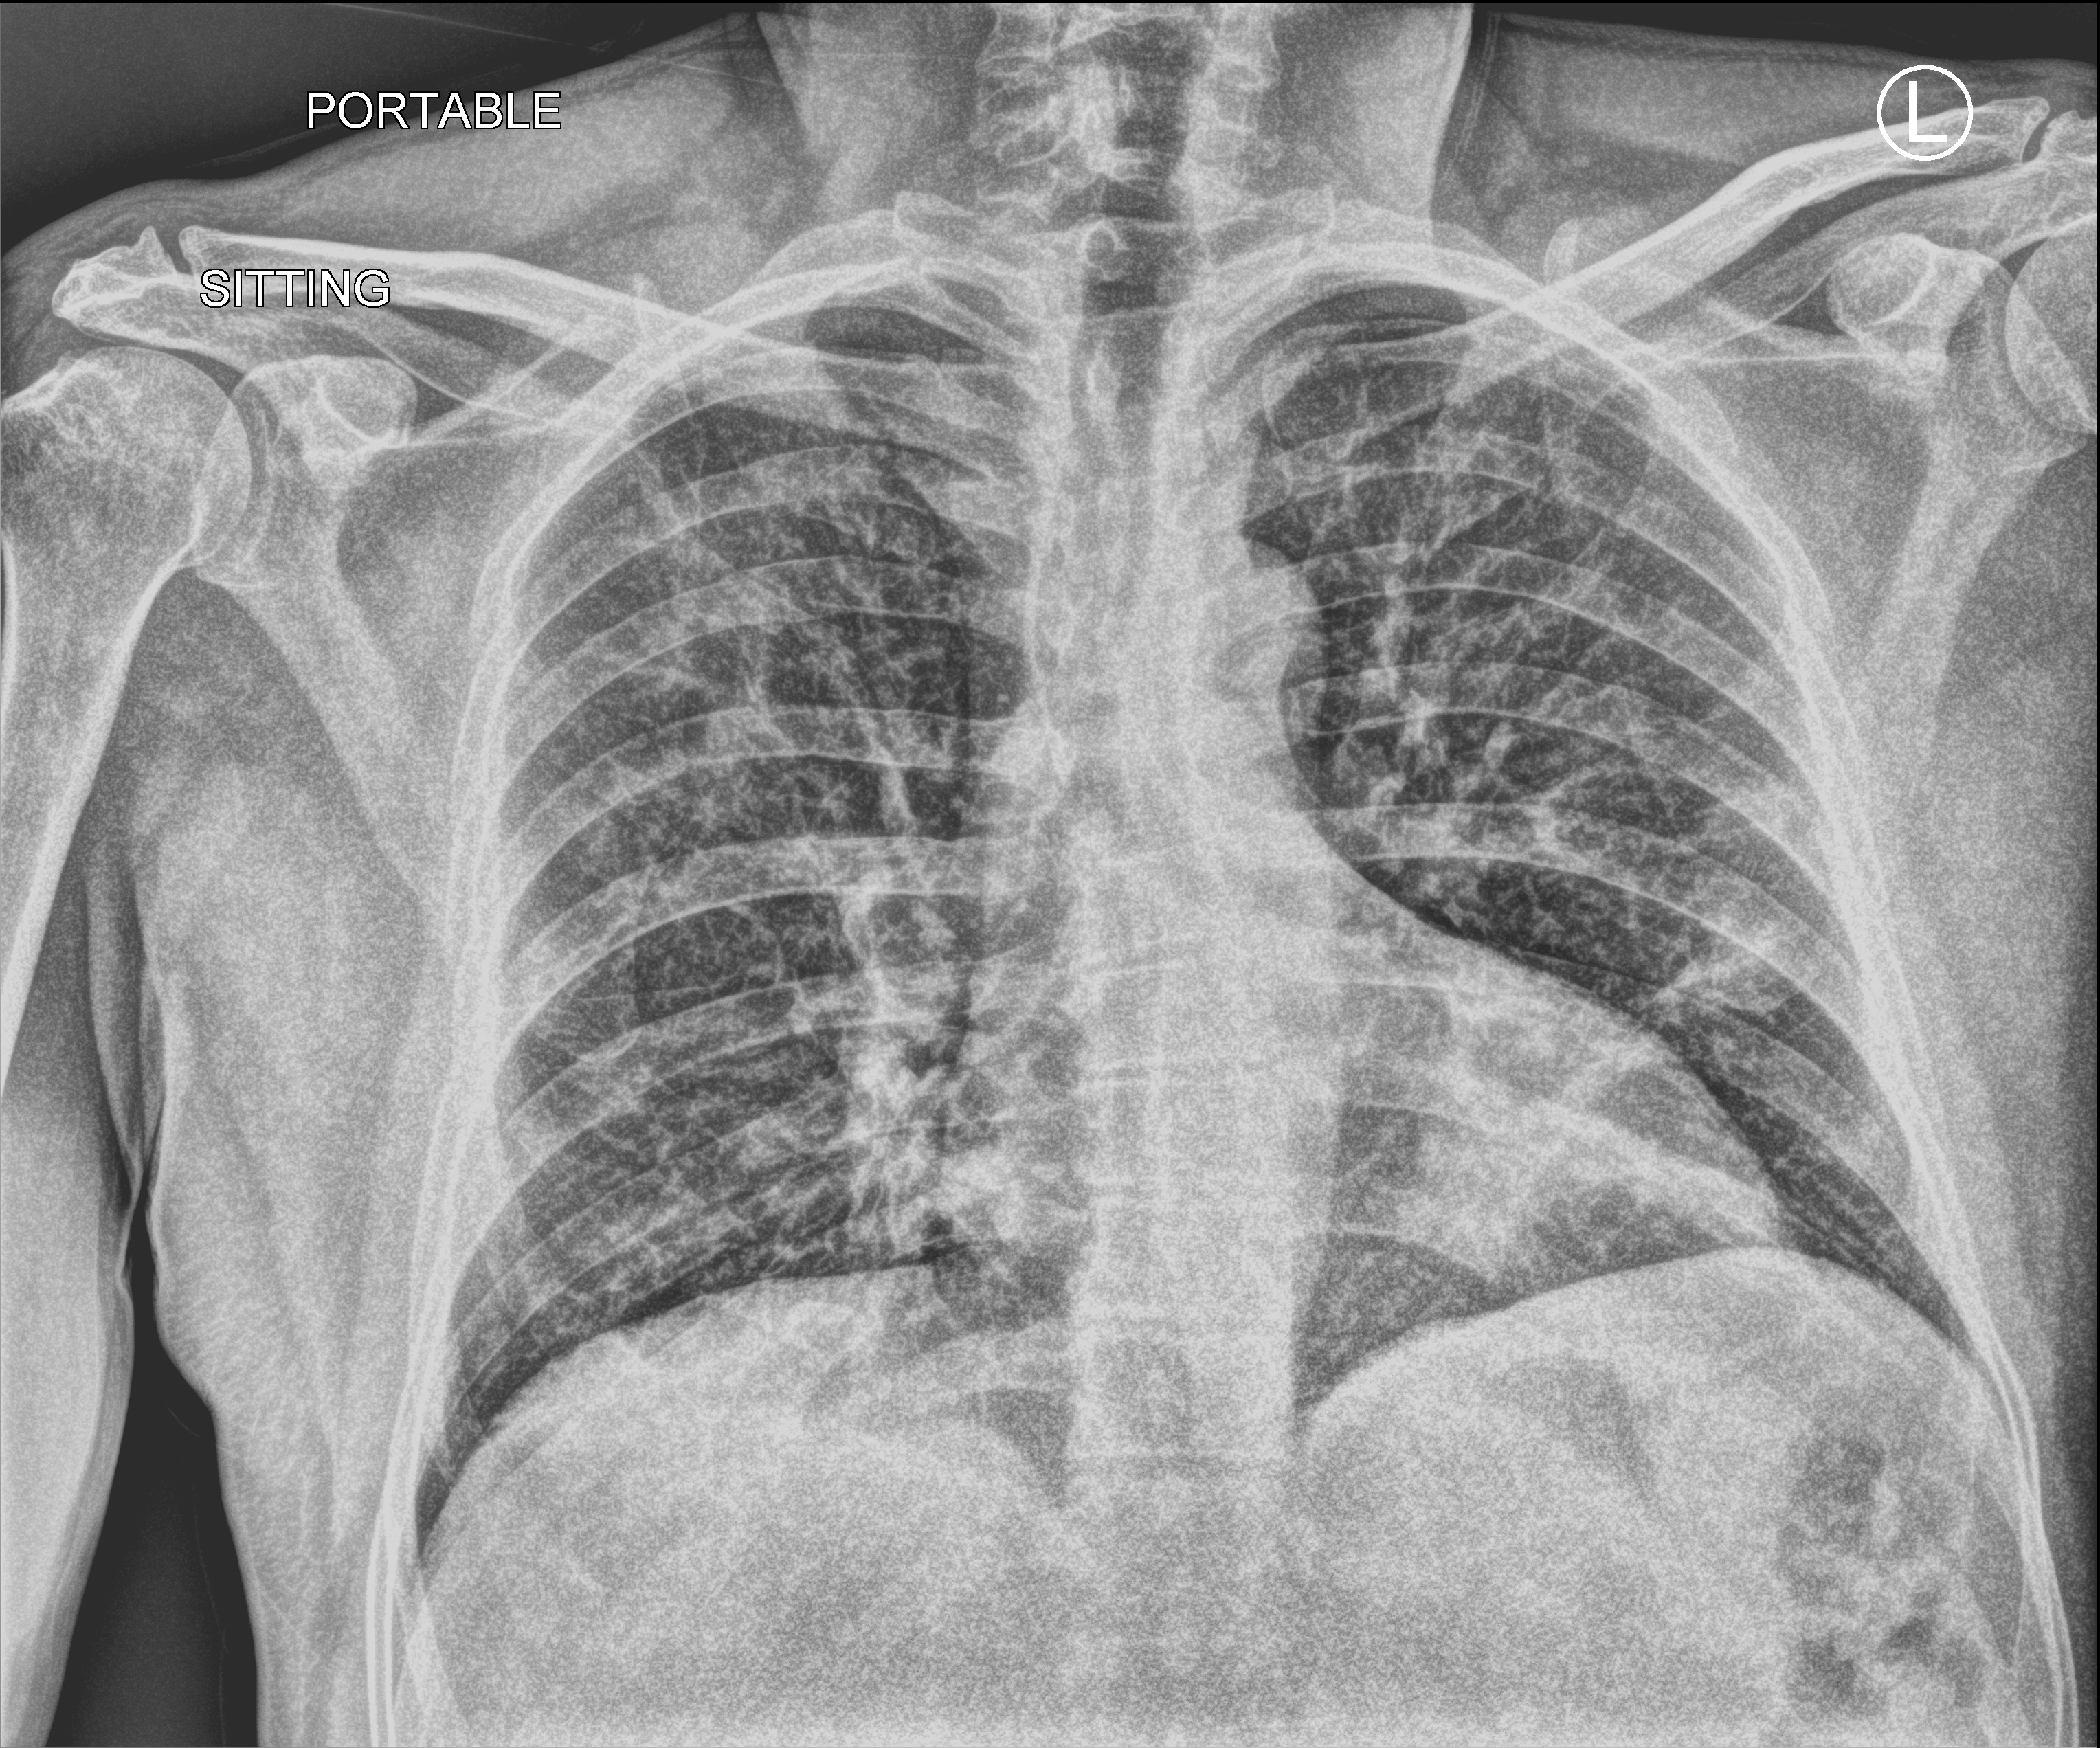
Portable chest radiograph; anteroposterior (AP) projection. Male patient hospitalised with COVID-19, age 18–59 years.
Admission-level facts for this patient (not findings on this image; timing relative to this image not recorded):
- length of hospital stay: 1 day
- admitted to intensive care during this hospital stay: no